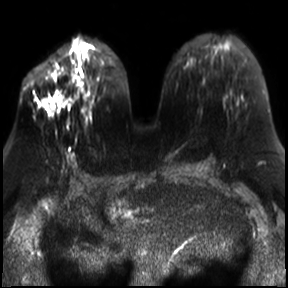
Breast MRI, one axial slice. Slice 14 of 30 in the series (ordered by position). Diffusion-weighted series; image 2 of 4 stored at this slice position (different b-values; order by instance number). 3 T. 288 × 288 image matrix, field of view 340 × 340 mm. Female patient.
Annotated regions visible in this slice (expert manual segmentation):
- tumour on diffusion-weighted imaging: bounding box [x1, y1, x2, y2] px = [43, 69, 79, 111]